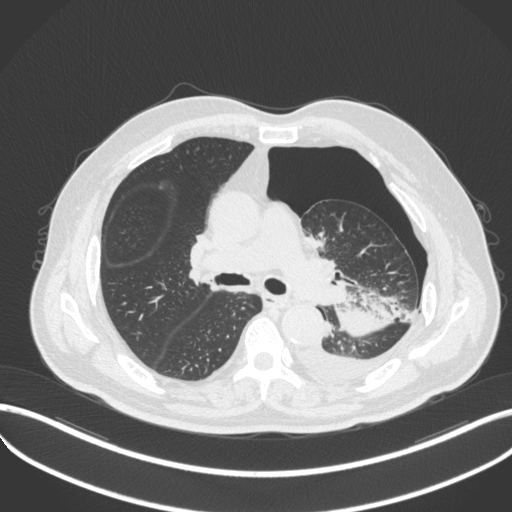
Chest CT, one axial slice; position 316 of 466 along the scan axis; reconstruction kernel B31f; 120 kVp; lung window (W 1500 / L -600 HU); 1 mm slice thickness; 512 × 512 image matrix, field of view 400 × 400 mm. Patient: male, 76 years. Case-level facts recorded for this patient, not image findings: clinical TNM (as recorded): T3 N0 M1b.
Outlined on this slice (rectangle marked by the reading radiologist):
- lung tumour (recorded histology: adenocarcinoma): bounding box <332,286,402,343> (left, top, right, bottom; pixels)